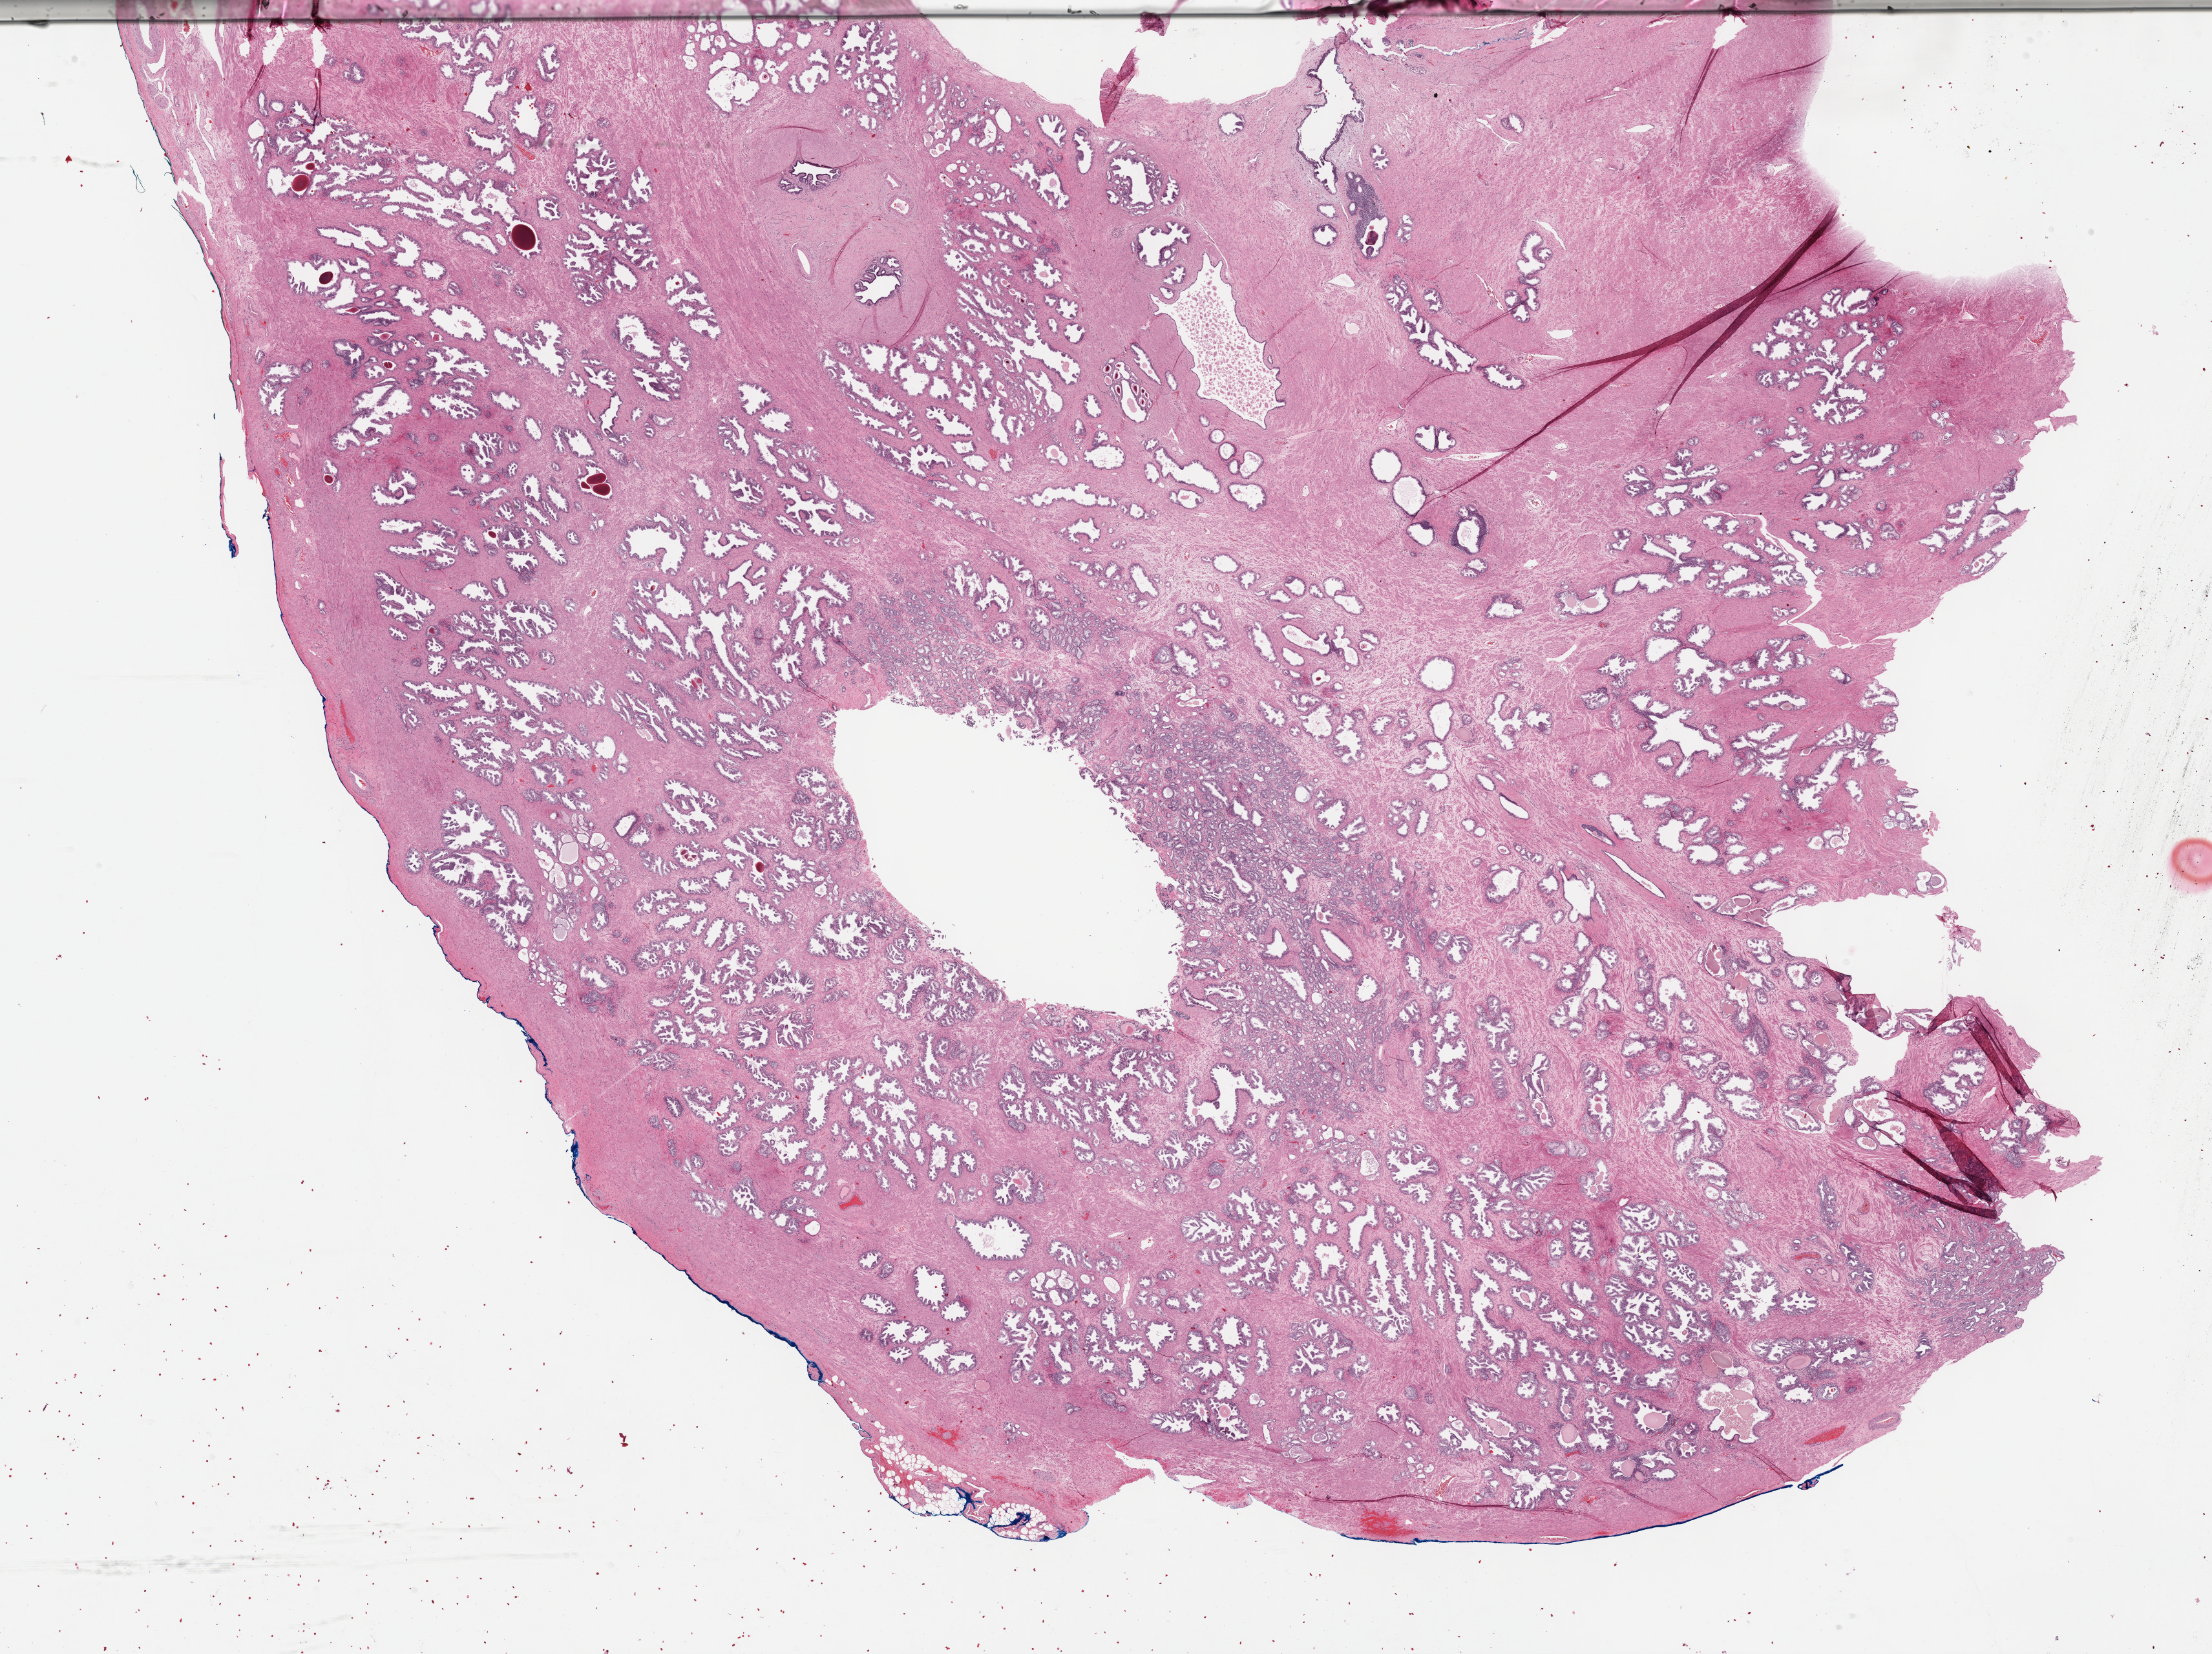
Whole-slide histology image, Hematoxylin and eosin (H&E) stained, whole scanned area (about 27.7 x 20.7 mm, slide scanned at 40x) shown as a low-resolution overview; formalin-fixed paraffin-embedded (FFPE) diagnostic section; prostate, primary tumour sample. Patient: male, age at initial diagnosis 51 years. Gleason score: 6 (3+3).
Lymph nodes positive (case pathology): 0 of 15 examined. Histologic diagnosis: Adenocarcinoma, NOS.